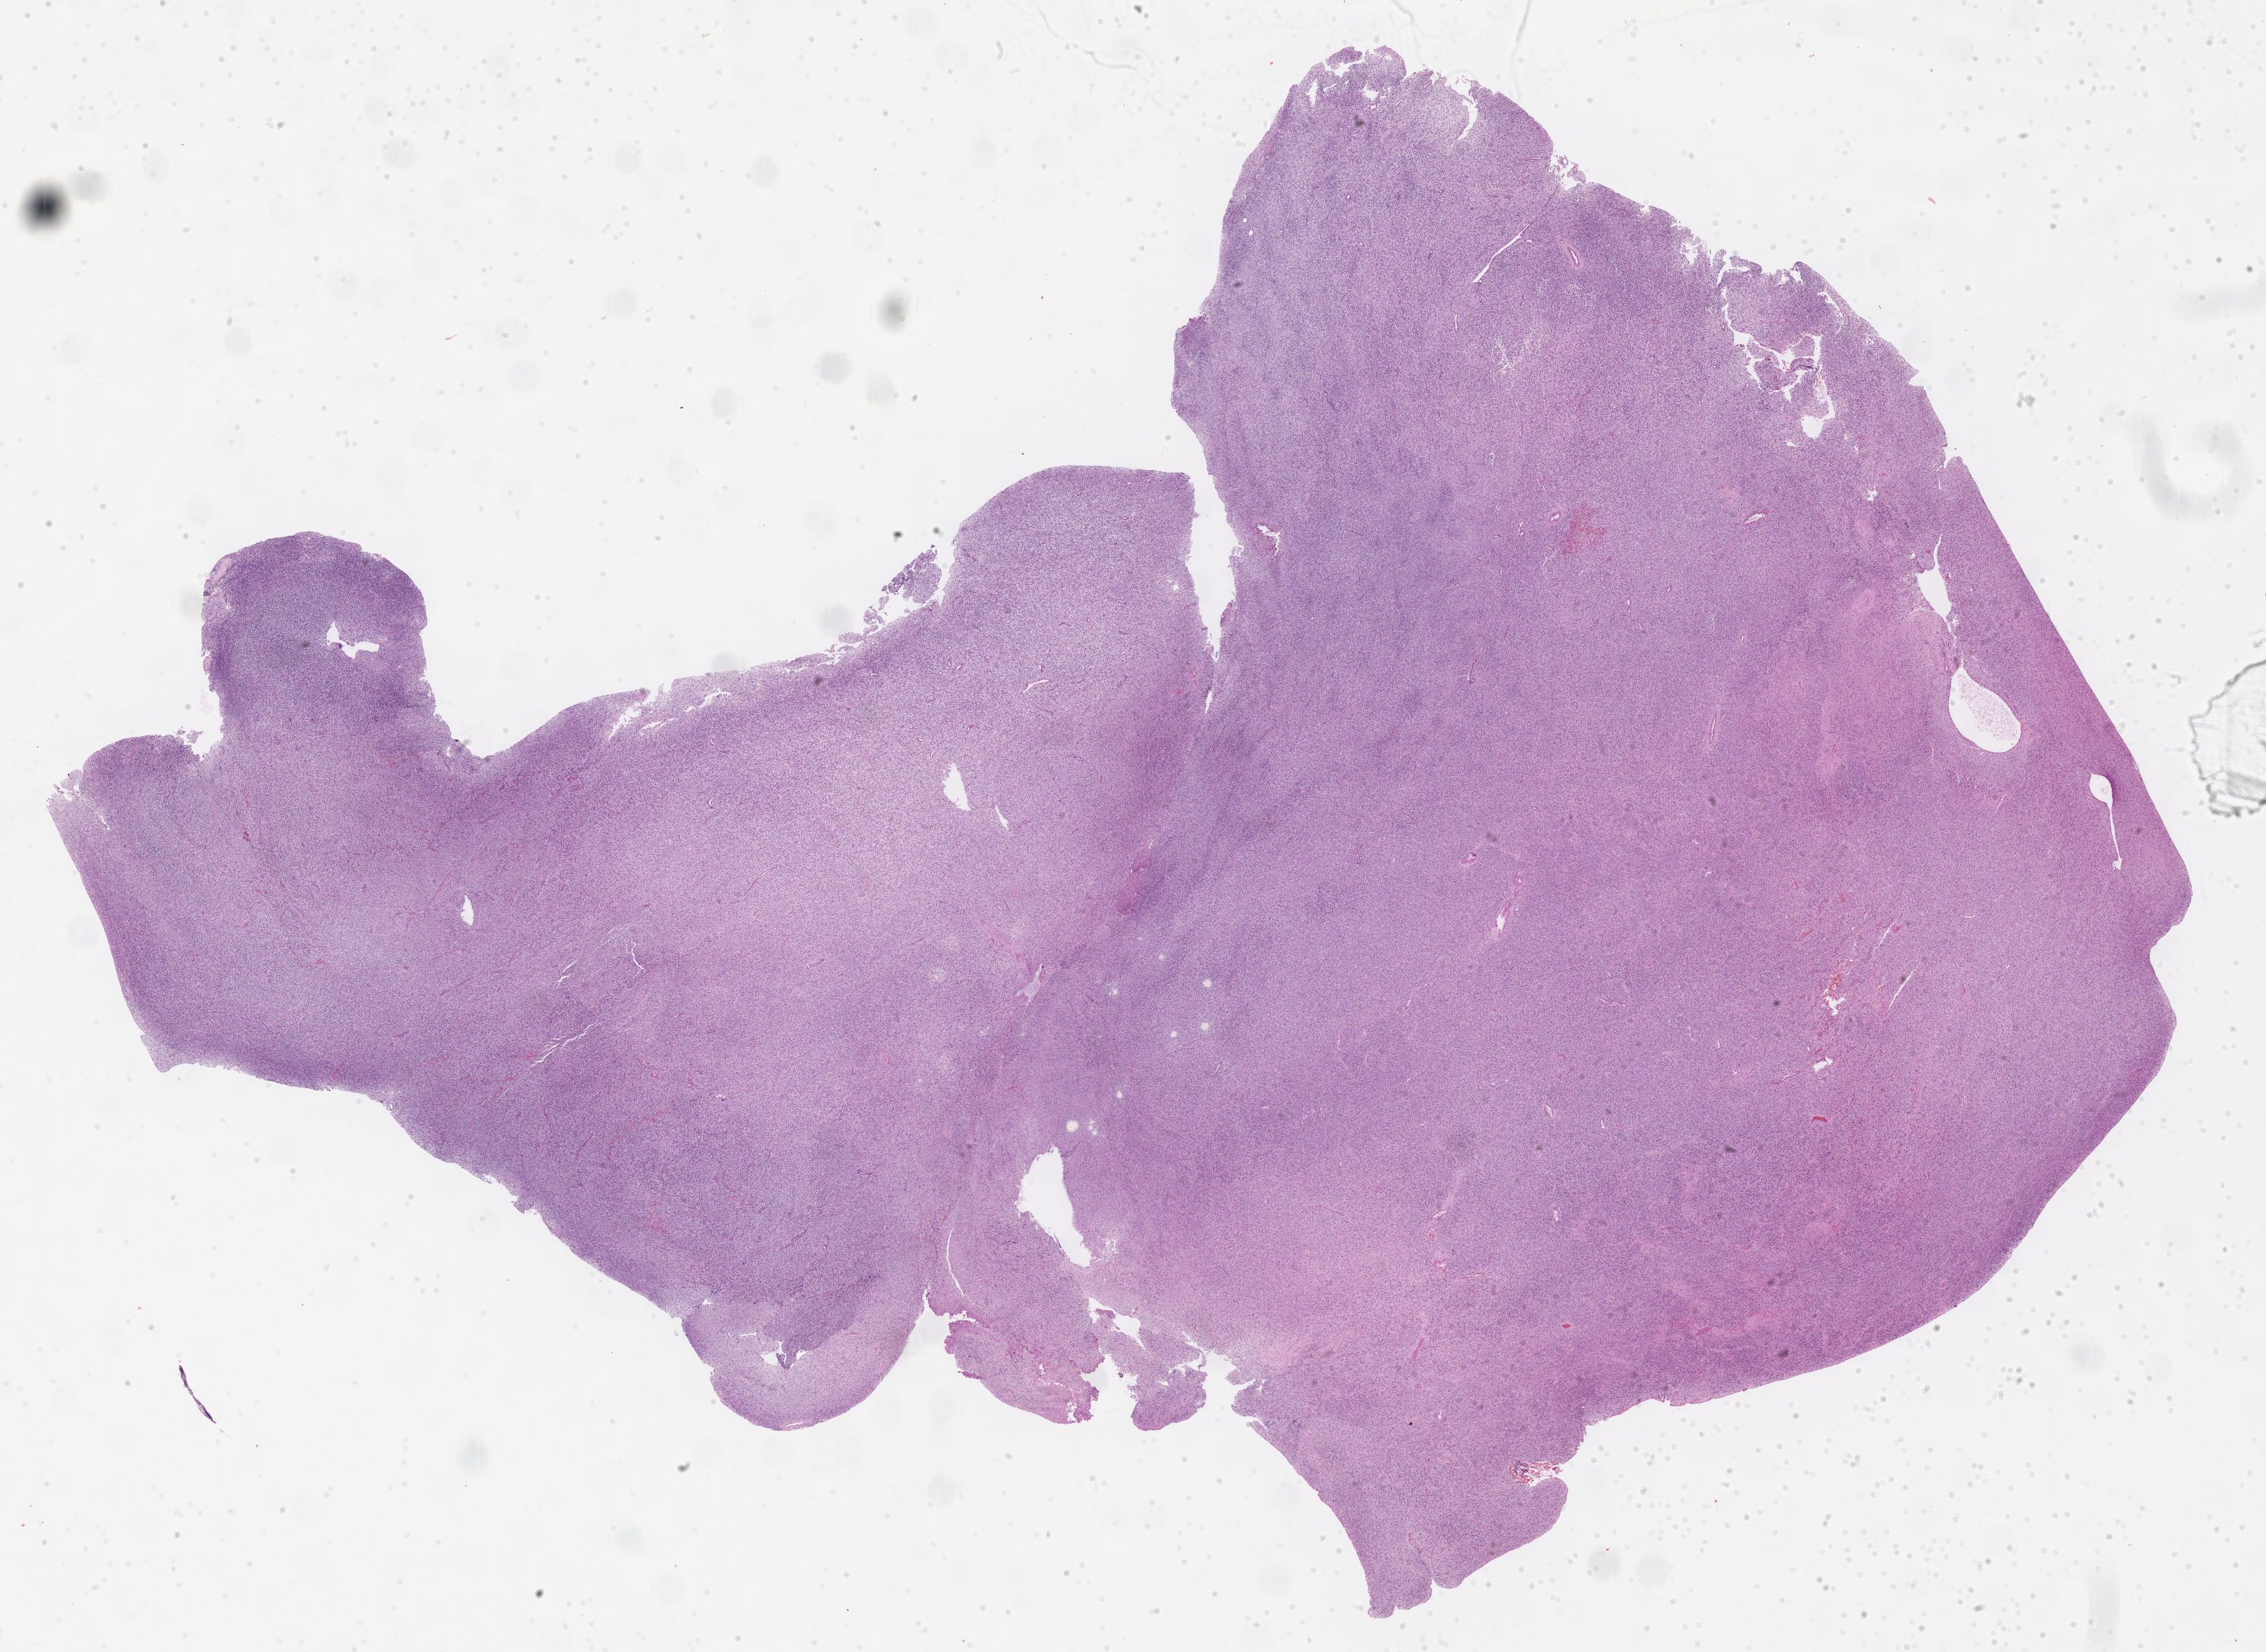
H&E whole-slide image of tumor tissue — low-resolution overview of the scanned area, about 26.2 x 19.1 mm. Formalin-fixed, paraffin-embedded (FFPE) tissue. Sample anatomic site: soft tissue, pelvis. Patient: male, age 1.3 years at diagnosis.
Primary site (case record): pelvis, Site Indeterminate. Stage (as recorded): 3. Metastatic status at presentation (as recorded): non-metastatic. Diagnosis: rhabdomyosarcoma; histological classification: embryonal rhabdomyosarcoma.